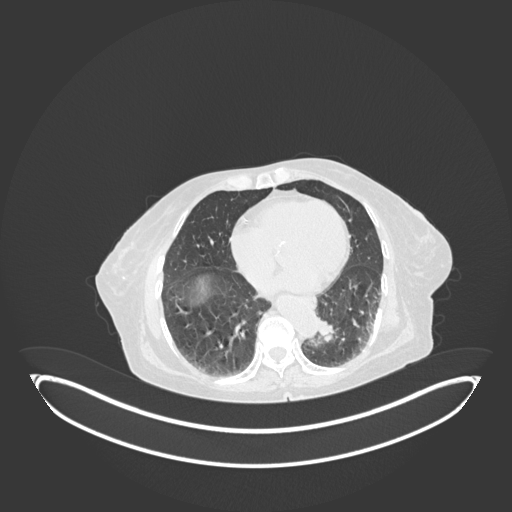
Chest CT, one axial slice; 120 kVp; lung window (W 1500 / L -600 HU); 512 × 512 image matrix. Patient: female, 82 years. From the clinical record (not read from this slice): clinical TNM (as recorded): T1b N0 M1.
Structures marked on this image (bounding box drawn by a radiologist):
- lung tumour (recorded histology: adenocarcinoma): bounding box (x1, y1, x2, y2) in pixels: (315, 312, 338, 345)